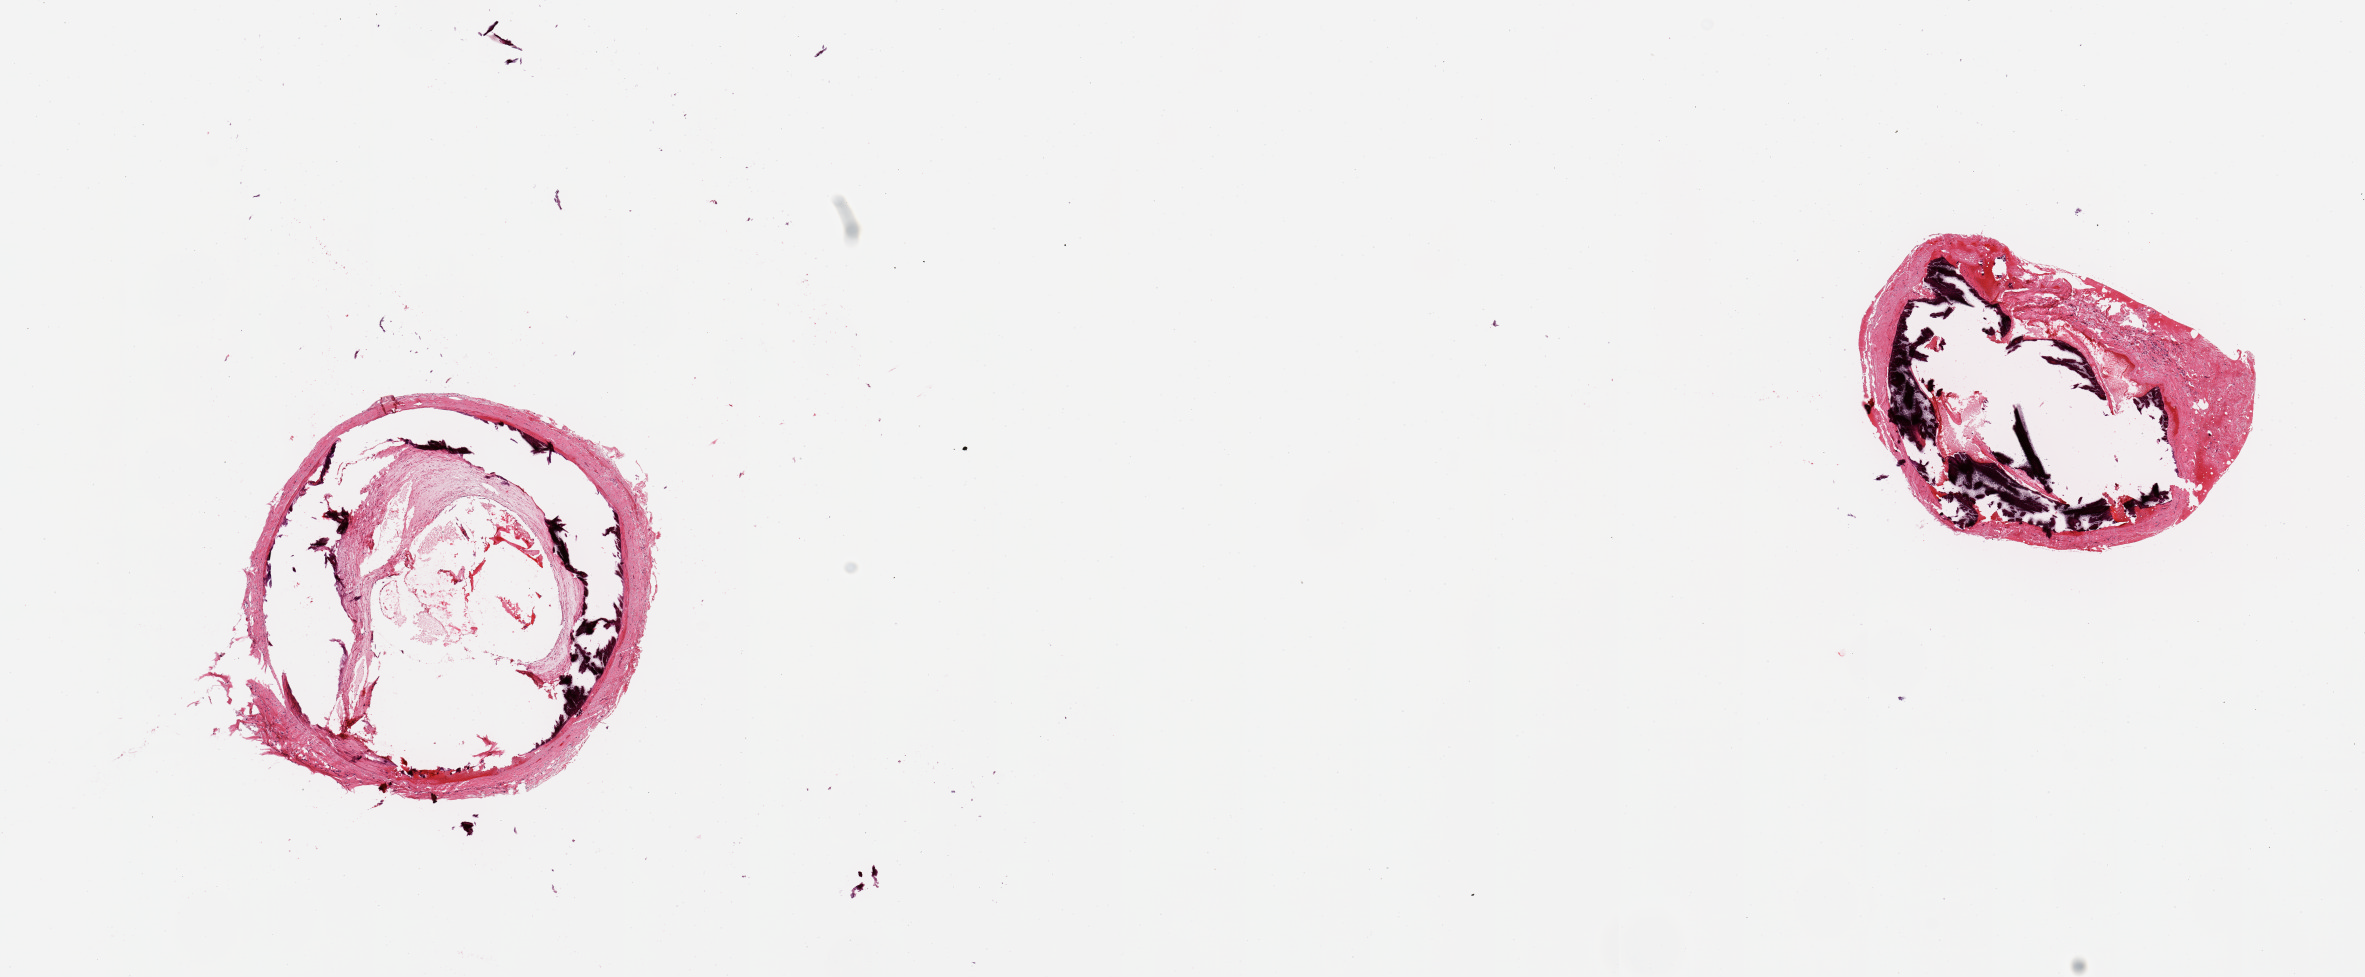
Hematoxylin and eosin (H&E) whole-slide image — a low-resolution overview of the entire scanned area, about 18.7 x 7.7 mm (acquisition: 20x scan); PAXgene-fixed paraffin-embedded (PFPE) section; target tissue: tibial artery; donor tissue sample. Female donor.
Review note (as recorded): 2 pieces ~70% occlusive atherosis, calcified.